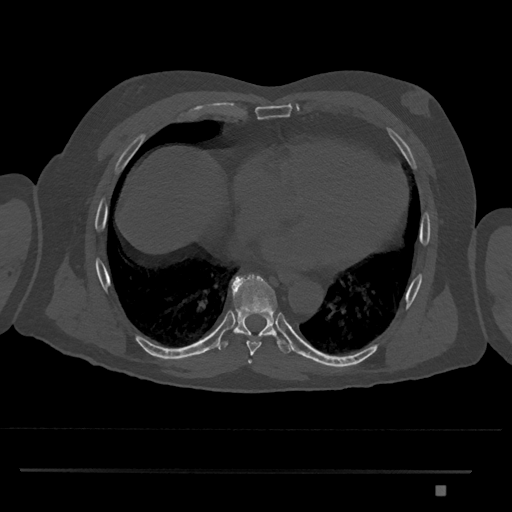
CT including the spine, one axial slice. Position 1133 of 1134 along the scan axis. Reconstruction kernel Br40s/3. Bone window (W 1800 / L 400 HU). 0.5 mm slice thickness. 512 × 512 image matrix, field of view 429 × 429 mm. Patient: male, 65 years. Case-level facts recorded for this patient, not image findings: primary cancer: prostate.
Annotated regions visible in this slice (semi-automatically segmented with operator editing):
- T8 vertebra: box from (x=216, y=275) to (x=292, y=355) px